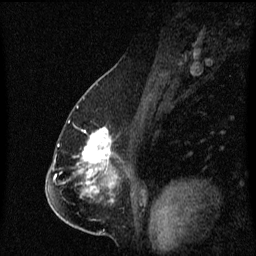
Breast MRI (dynamic contrast-enhanced), one sagittal slice; slice 37 of 60 in the series (ordered by position); dynamic contrast-enhanced series, image 2 of 3 at this slice position (ordered by acquisition); 1.5 T; TE 4.2 ms, TR 8.4 ms; 2 mm slice thickness; 256 × 256 image matrix. Female patient, age 57 years. From the clinical record (not read from this slice): setting: breast cancer imaged before/during neoadjuvant chemotherapy; receptor status: HR-positive, HER2-negative.
Outlined on this slice (semi-automatic segmentation, software-assisted and operator-edited):
- analysis volume of interest (the breast-tissue region the enhancement analysis was run in; not a lesion): bounding box [x1, y1, x2, y2] px = [67, 120, 123, 177]
- tumour enhancement mask (voxels above the 70 % enhancement threshold inside the analysis volume of interest): [82, 128, 111, 169]